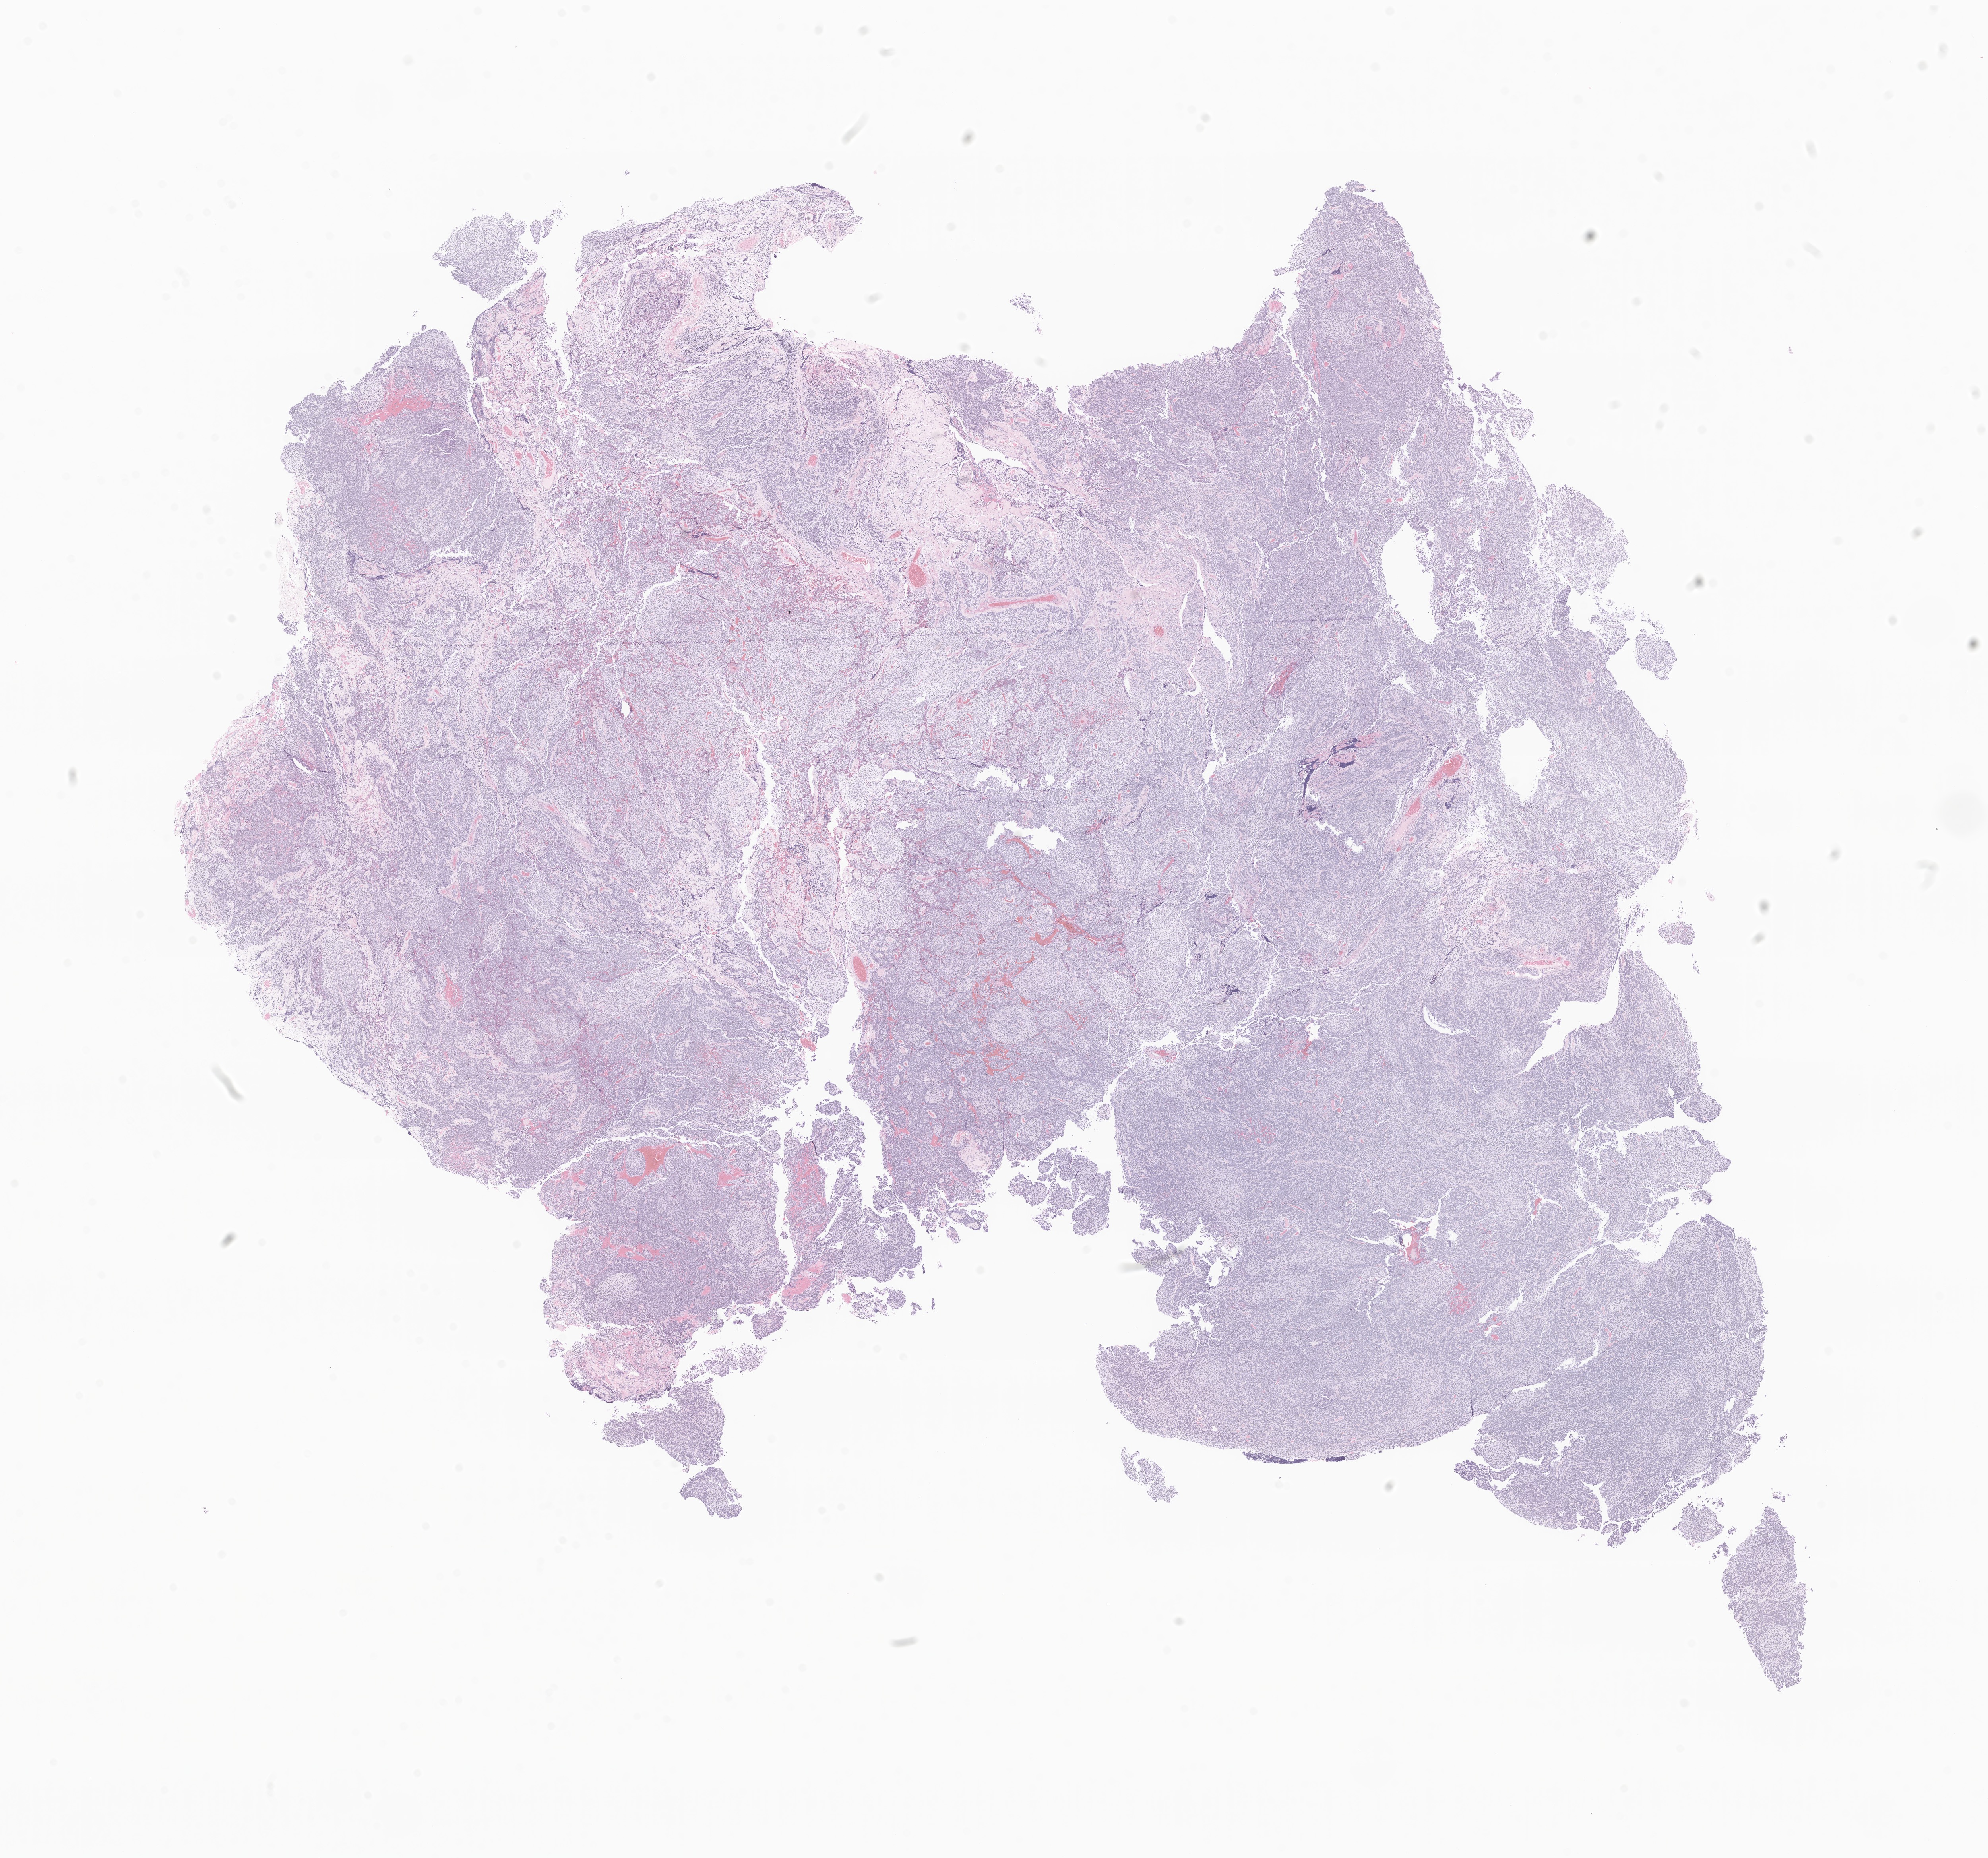
Whole-slide image, H&E stain of tumor tissue from the brain, whole scanned area (about 21.1 x 19.7 mm) shown as a low-resolution overview. FFPE section. Male patient, age 99 months (8 years 3 months).
Diagnosis: Medulloblastoma, NOS.